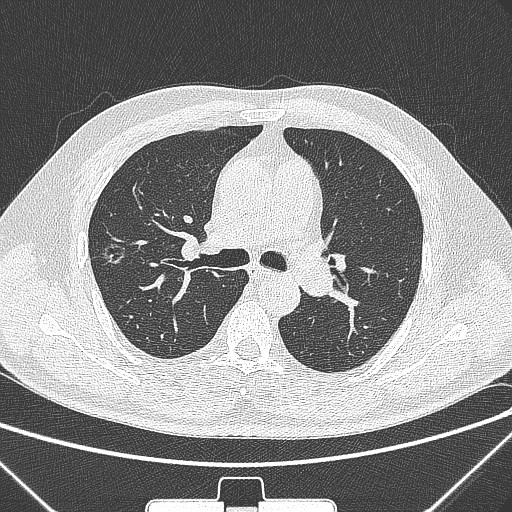
Chest CT, one axial slice. Position 194 of 320 along the scan axis. Lung window (W 1500 / L -600 HU). 1 mm slice thickness. 512 × 512 image matrix. Patient: male, 58 years. Case-level facts recorded for this patient, not image findings: clinical TNM (as recorded): T1c N0 M0.
Annotated regions visible in this slice (bounding box drawn by a radiologist):
- lung tumour (recorded histology: adenocarcinoma): bounding box [x1, y1, x2, y2] px = [95, 232, 128, 272]